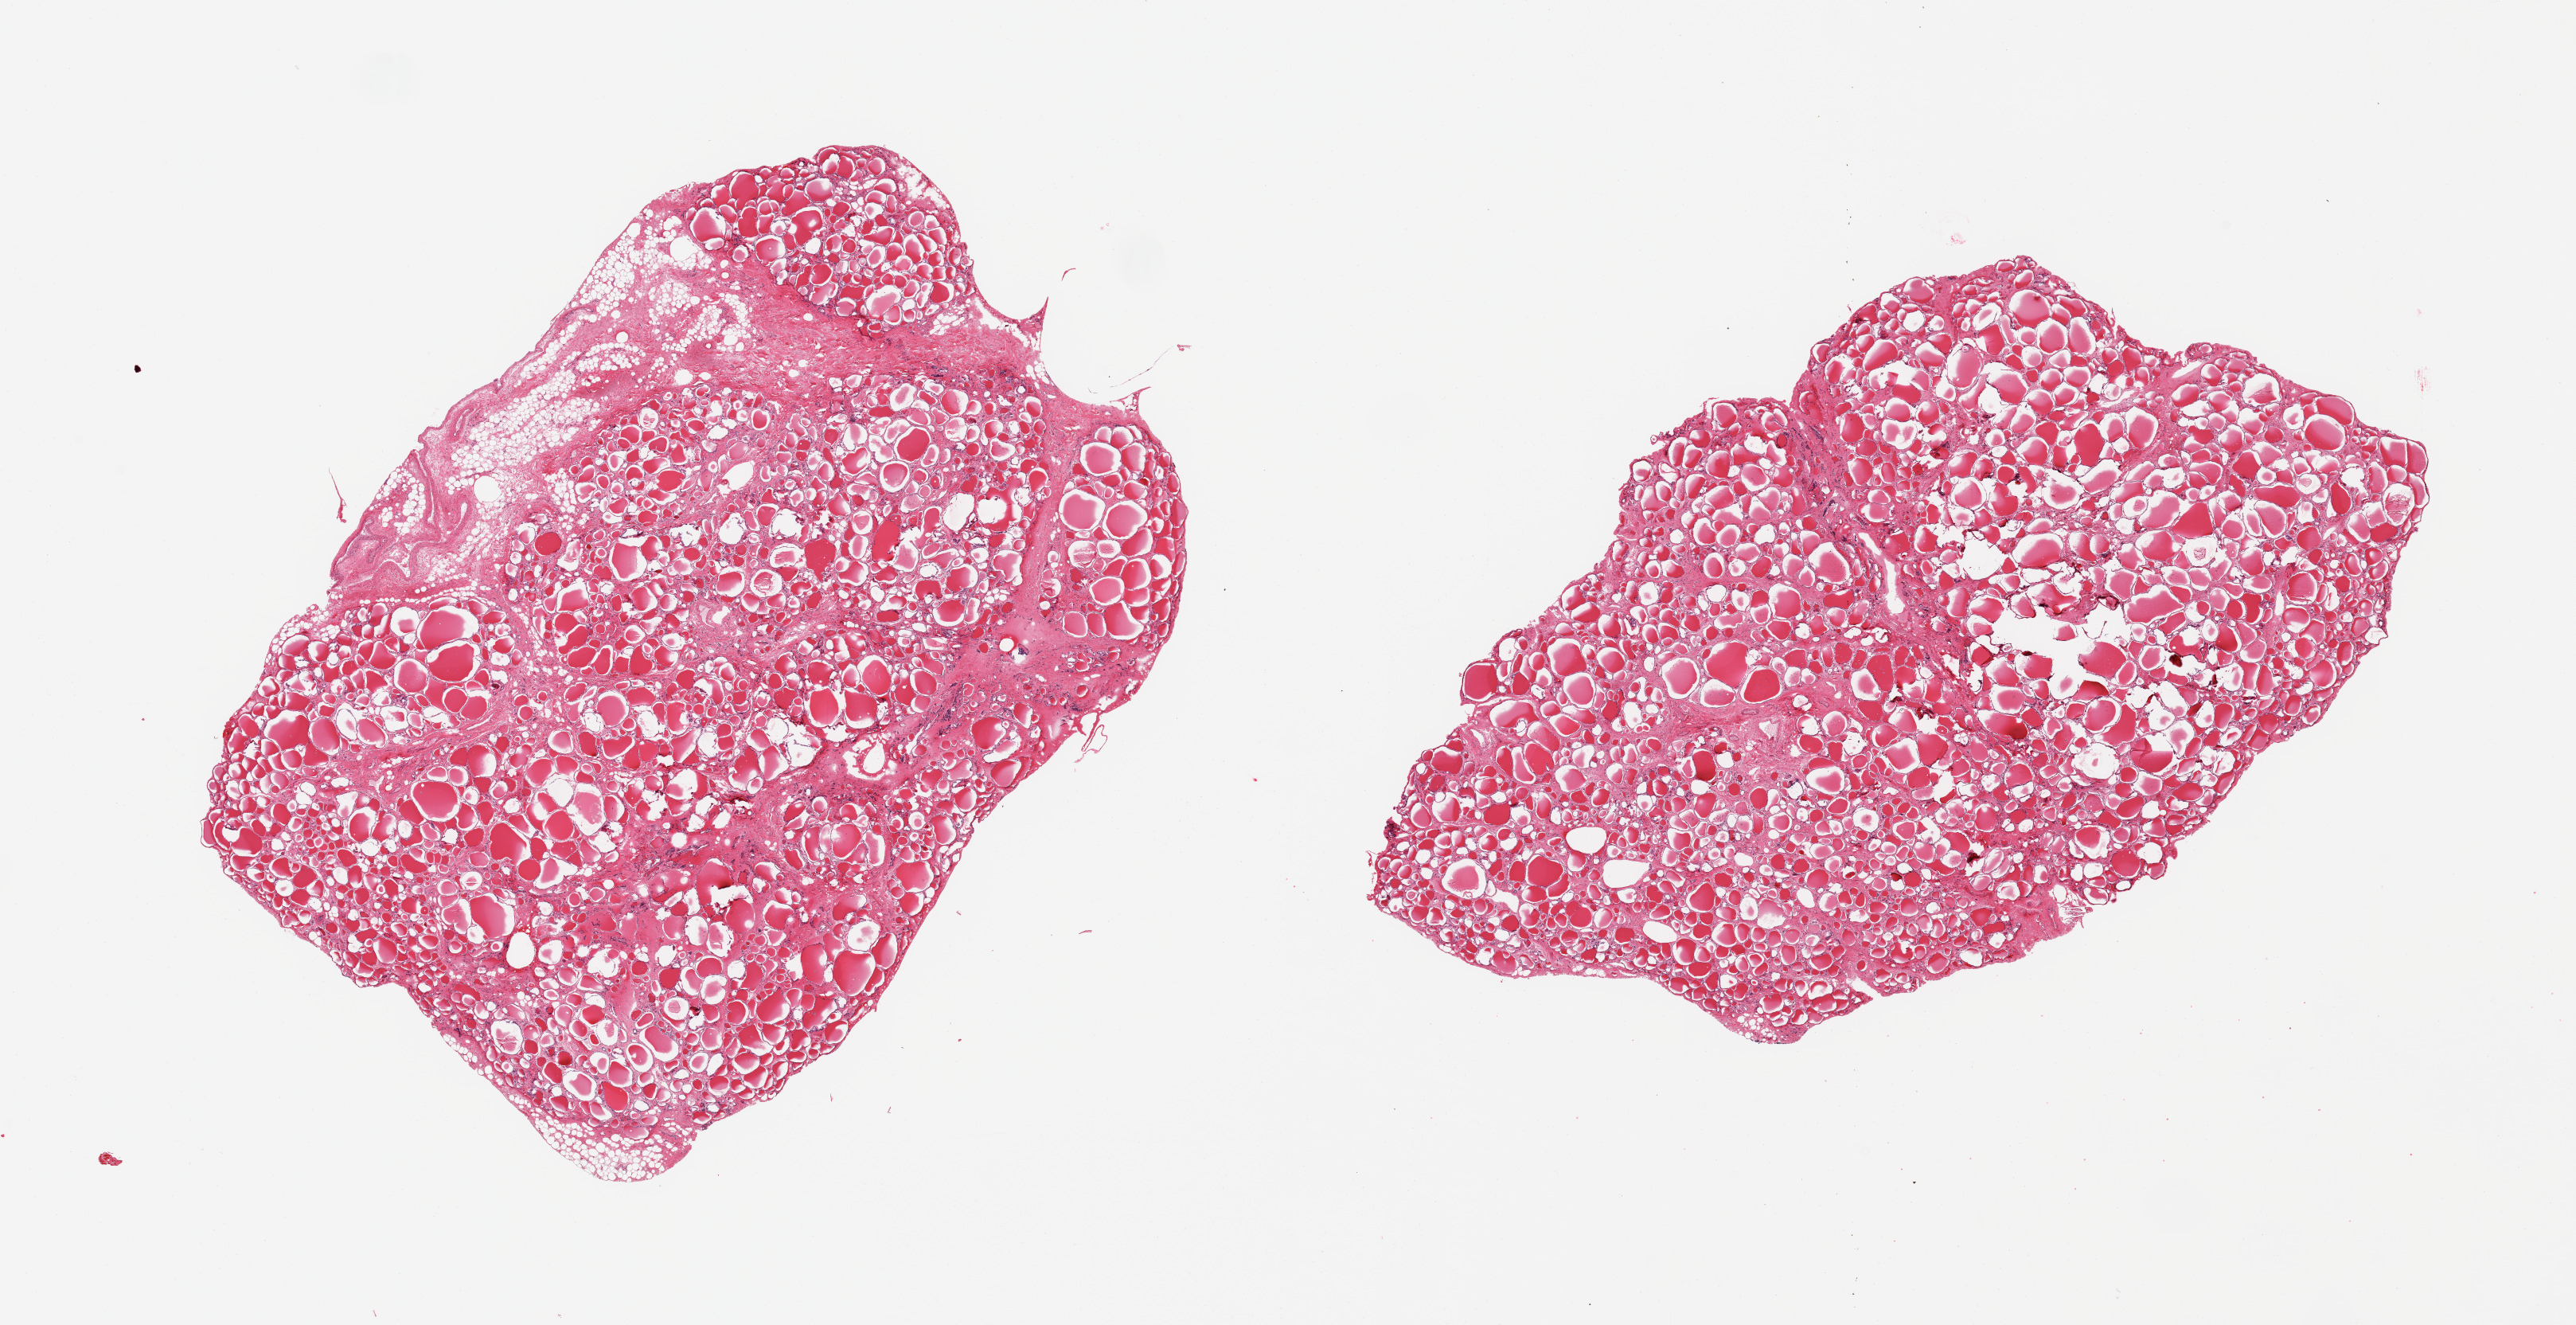
H&E whole-slide image, brightfield, a low-resolution overview of the entire scanned area, about 25.6 x 13.2 mm; PAXgene-fixed paraffin-embedded (PFPE) section; section of thyroid (target tissue); donor tissue sample. Male donor.
Review note (as recorded): 2 pieces, no abnormalities; nubbin of adherent fibroadipose tissue up to ~1mm.